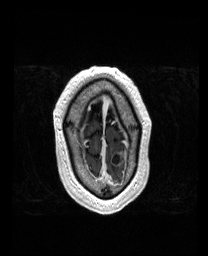
Brain MRI from a brain-tumour surgery series, one axial slice; T1-weighted post-contrast; 208 × 256 image matrix, field of view 211 × 260 mm. From the clinical record (not read from this slice): histopathology: Metastatic Carcinoma from Lung Adenocarcinoma.
Structures marked on this image (expert manual segmentation):
- tumour: bounding box (x1, y1, x2, y2) in pixels: (113, 155, 123, 164)